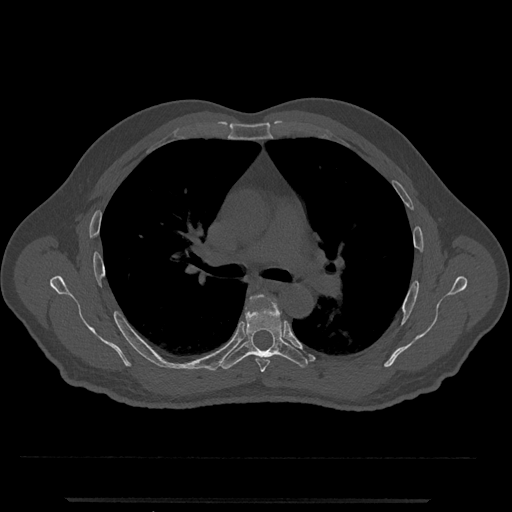
CT including the spine, one axial slice; slice 758 of 797 in the series (ordered by position); bone window (W 1800 / L 400 HU); 0.5 mm slice thickness; 512 × 512 image matrix, field of view 419 × 419 mm. Patient: male, 63 years. Case-level facts recorded for this patient, not image findings: primary cancer: prostate.
Outlined on this slice (semi-automatically segmented with operator editing):
- T5 vertebra: box from (x=246, y=302) to (x=270, y=373) px
- T6 vertebra: (x=220, y=295)–(x=308, y=370)